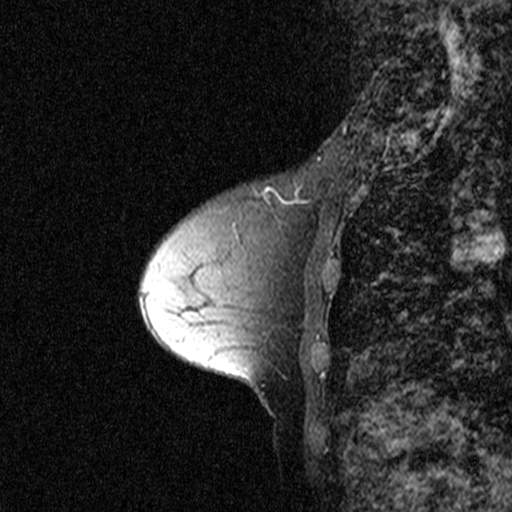
Breast MRI (dynamic contrast-enhanced), one sagittal slice; slice 18 of 44 in the series (ordered by position); dynamic contrast-enhanced study with each time point stored as its own series, time point 2 of 3 at this slice position (early post-contrast, ordered by acquisition time); 1.5 T; TE 4.5 ms, TR 11 ms; 2.27 mm slice thickness; 512 × 512 image matrix, field of view 200 × 200 mm. Patient: female, 53 years. Case-level facts recorded for this patient, not image findings: setting: breast cancer imaged before/during neoadjuvant chemotherapy; receptor status: HR-positive, HER2-negative.
Structures marked on this image (semi-automatic segmentation, software-assisted and operator-edited):
- analysis volume of interest (the breast-tissue region the enhancement analysis was run in; not a lesion): bounding box (x1, y1, x2, y2) in pixels: (200, 178, 317, 309)
- tumour enhancement mask (voxels above the 90 % enhancement threshold inside the analysis volume of interest): (265, 189, 310, 204)